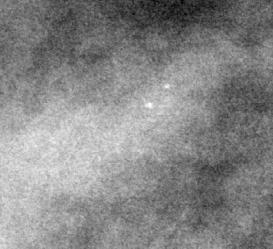
Region of interest cut from a scanned film mammogram (one marked finding); right breast; MLO view; BI-RADS breast density category 3 (scale 1–4).
- Finding: calcifications, morphology punctate, distribution clustered; BI-RADS assessment category 4; subtlety rating 3 on a 1 (subtle) to 5 (obvious) scale; pathology (as recorded): benign.